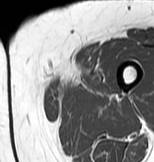
MRI of an extremity soft-tissue mass, one axial slice. Position 5 of 83 along the scan axis. MR volume resampled by the dataset authors to the PET/CT grid (not the native acquisition matrix). 3.27 mm slice thickness. 154 × 162 image matrix. Female patient. From the clinical record (not read from this slice): histological type: myxofibrosarcoma; grade: intermediate; site of the primary tumour: left thigh.
Outlined on this slice (expert contour drawn on MRI and transferred to this co-registered scan by the dataset authors):
- gross tumour volume including surrounding oedema: bounding box <49,66,109,99> (left, top, right, bottom; pixels)